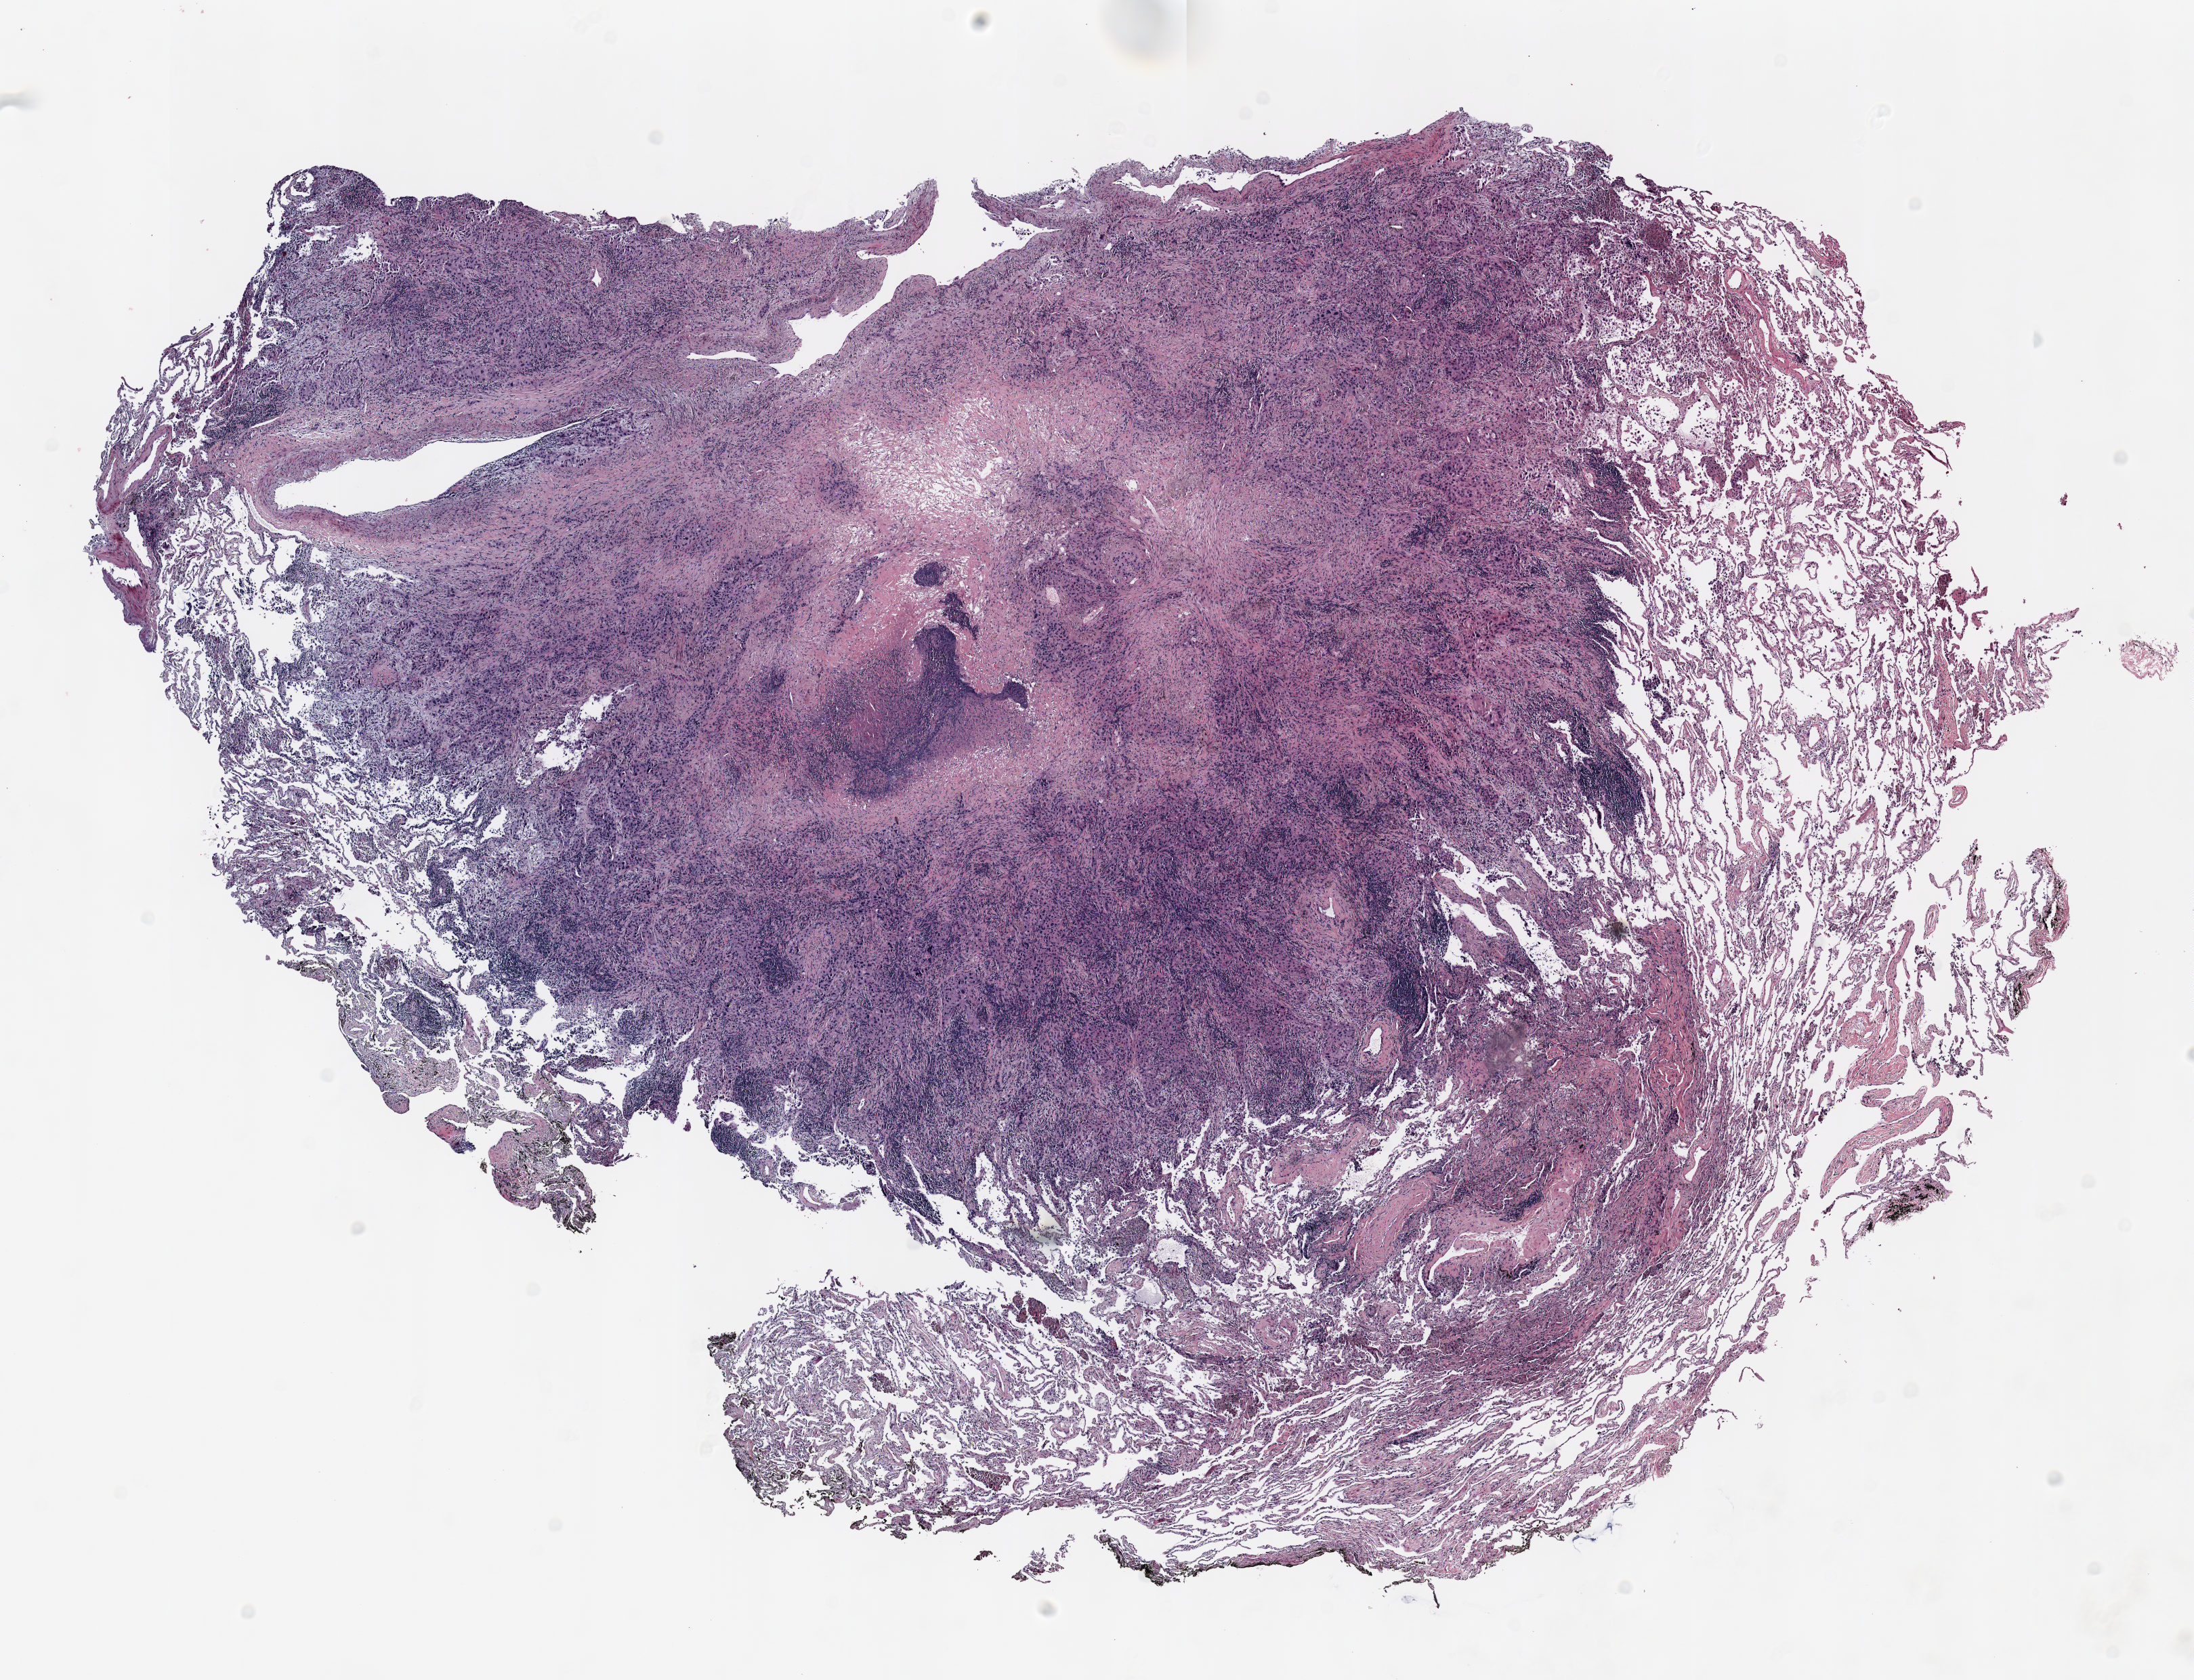
Whole-slide histology image, H&E-stained — low-resolution overview of the scanned area, about 13.0 x 10.0 mm (acquisition: 20x scan); FFPE section; lung tissue. Female patient, aged 72 at enrolment. Grade: poorly differentiated (G3).
Tumour size (pathology): 9 mm. Stage (AJCC 6th edition): IA. Primary tumour location (clinical record): right upper lobe. Participant's lung-cancer diagnosis: Non-small cell carcinoma (ICD-O-3 8046/3).